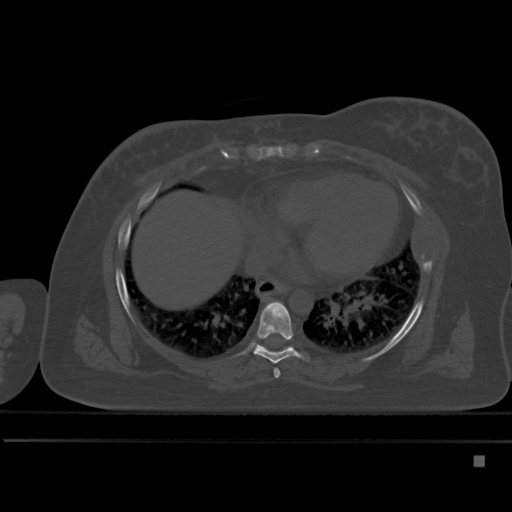
CT including the spine, one axial slice. Slice 290 of 495 in the series (ordered by position). Bone window (W 1800 / L 400 HU). 1.5 mm slice thickness. 512 × 512 image matrix. Patient: female, 33 years. Case-level facts recorded for this patient, not image findings: primary cancer: breast; vertebrae with lytic lesions (as recorded): T1.
Annotated regions visible in this slice (semi-automatic segmentation, software-assisted and operator-edited):
- T6 vertebra: bounding box [x1, y1, x2, y2] px = [274, 369, 280, 378]
- T7 vertebra: [253, 301, 302, 364]
- T8 vertebra: [255, 344, 293, 350]